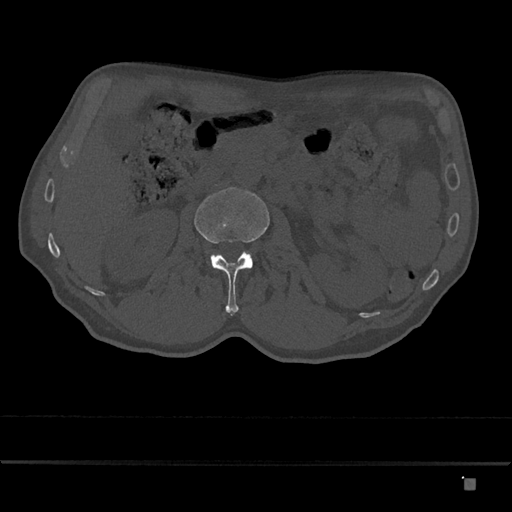
CT including the spine, one axial slice. Slice 467 of 797 in the series (ordered by position). Reconstruction kernel Br40s/3. Bone window (W 1800 / L 400 HU). 512 × 512 image matrix, field of view 390 × 390 mm. Male patient, age 72 years. From the clinical record (not read from this slice): primary cancer: prostate.
Structures marked on this image (semi-automatic segmentation, software-assisted and operator-edited):
- L2 vertebra: box from (x=194, y=187) to (x=270, y=316) px